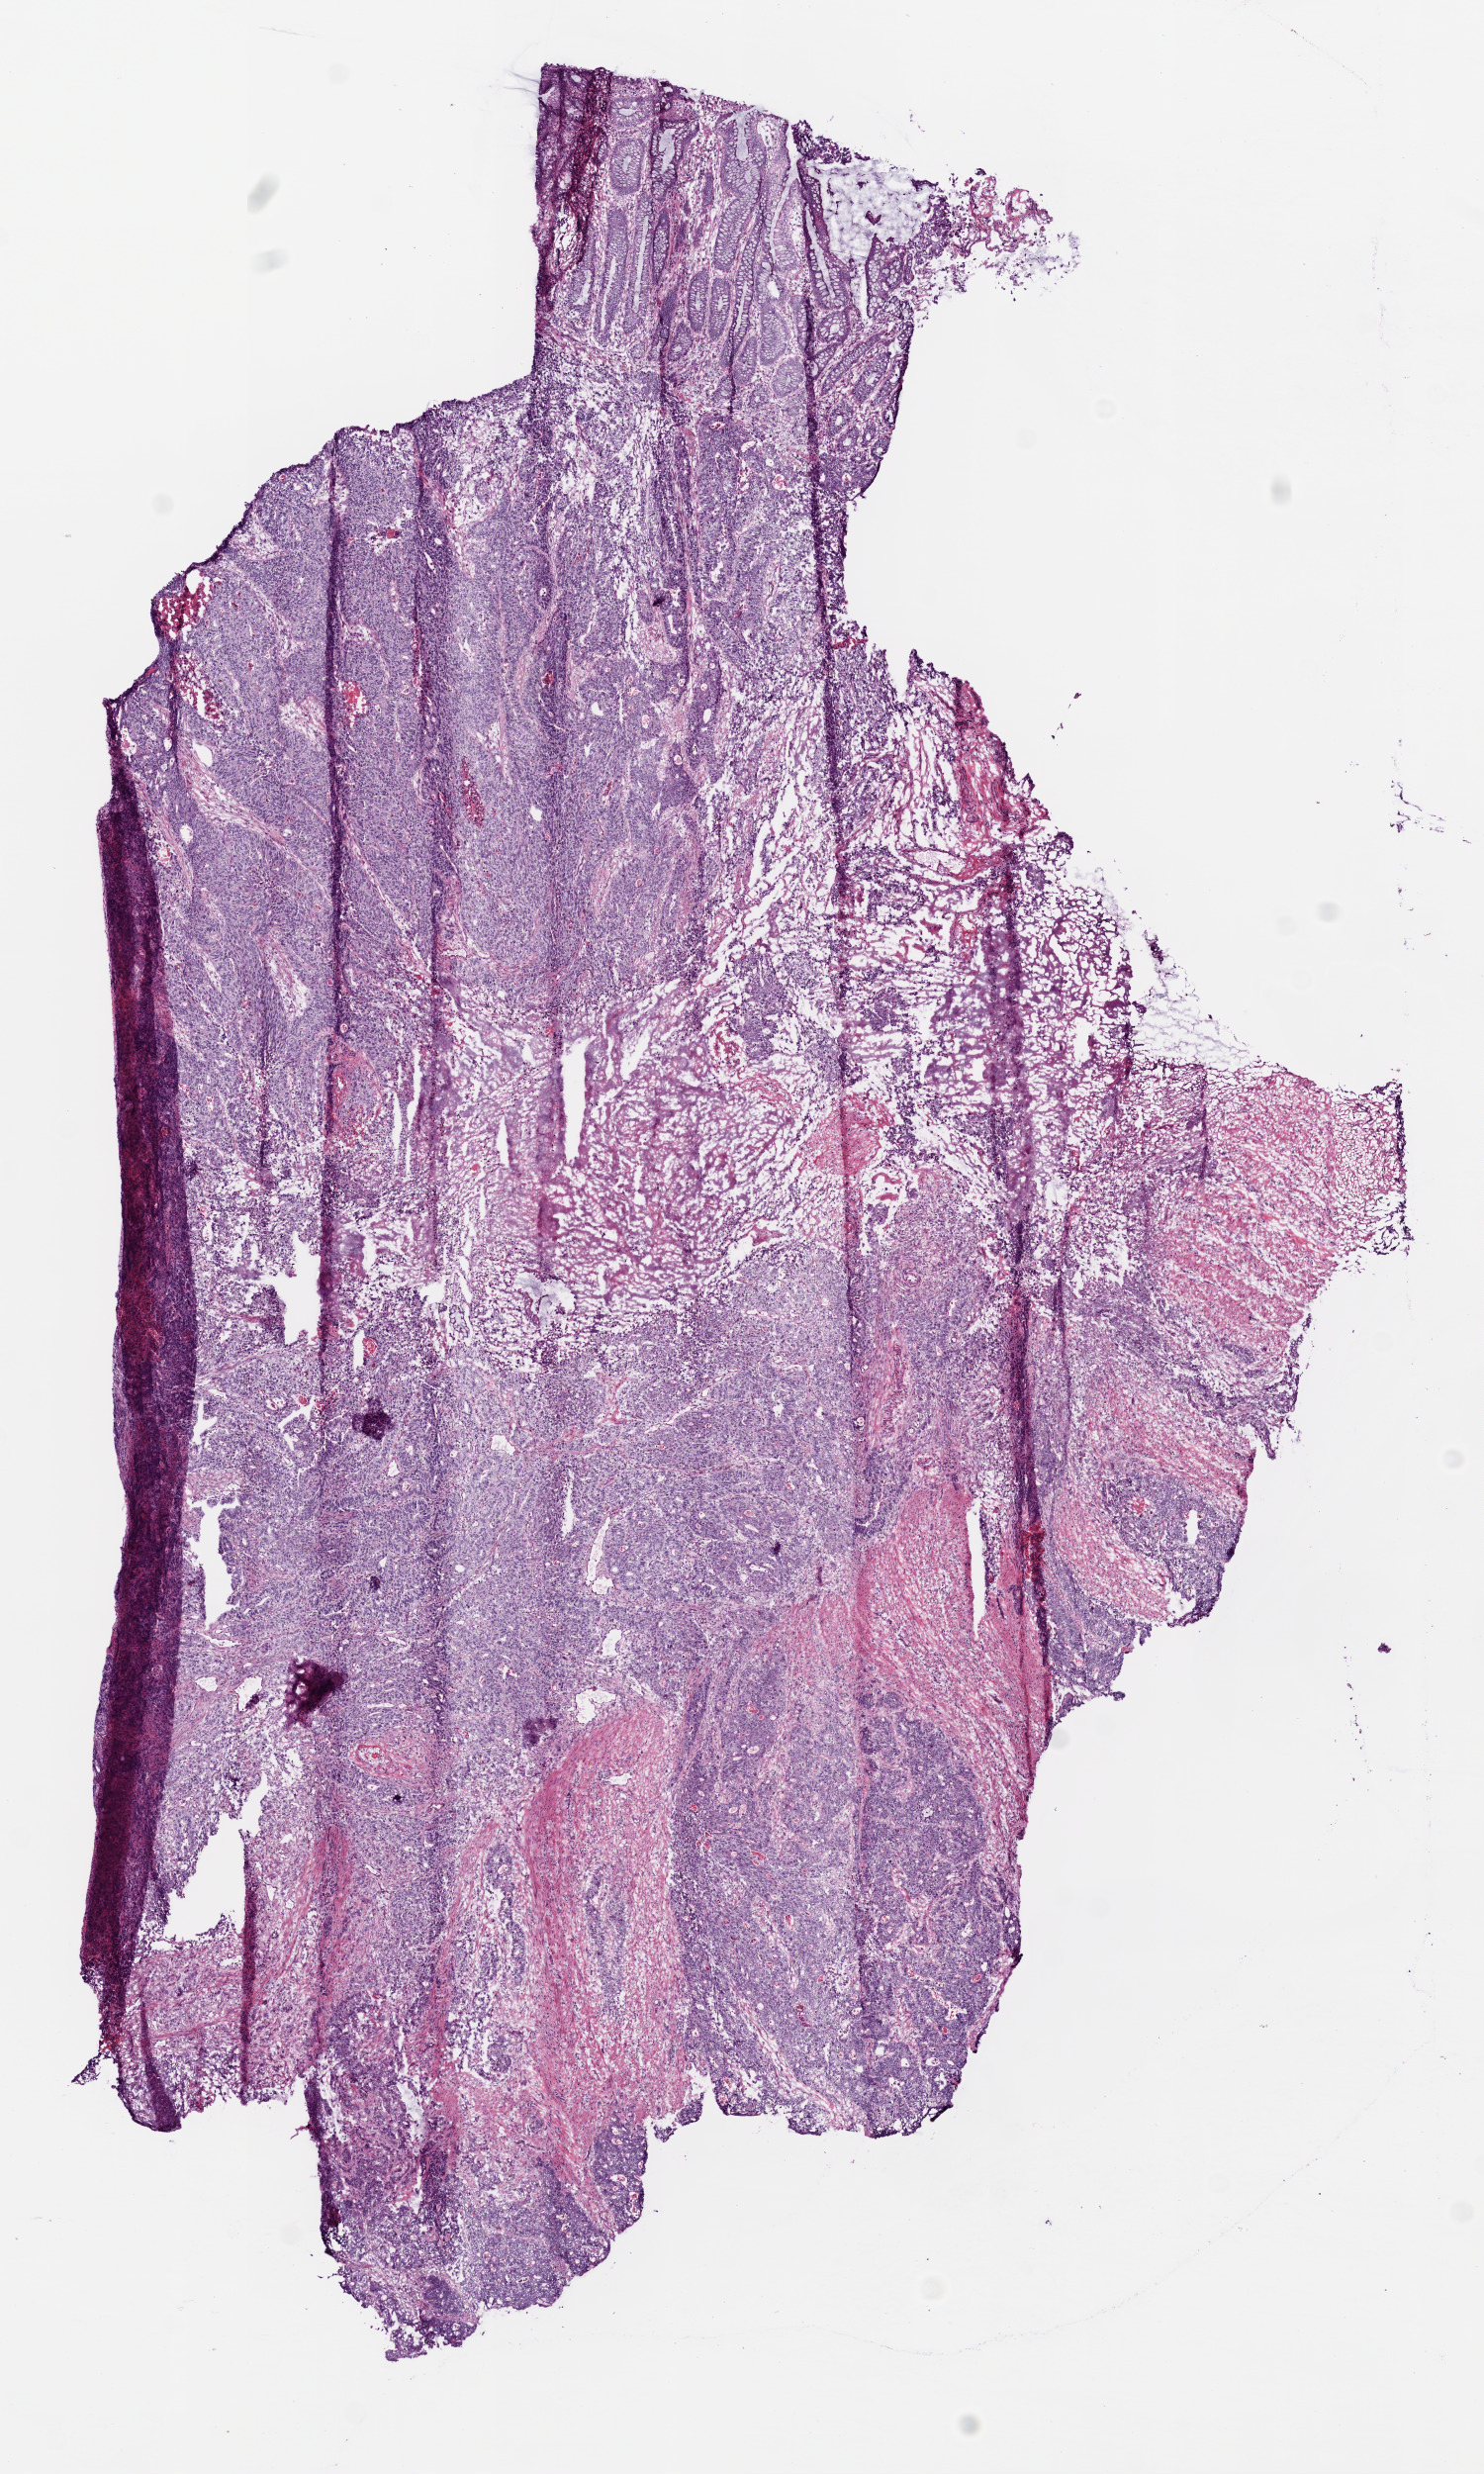
Digitized H&E-stained tissue section (whole slide) — low-resolution overview of the scanned area, about 6.0 x 10.0 mm (from a 20x scan). Frozen section from the bottom of the tissue portion. Primary tumour sample from the rectum. Female patient; age at initial diagnosis 61 years. Composition of this section per pathologist review: tumour cells 65%, tumour nuclei 75%, normal cells 10%, stromal cells 20%, necrosis 5%.
TNM: T3 N2 M0. Diagnosis: Adenocarcinoma, NOS (rectosigmoid junction). AJCC pathologic stage: IIIC (6th edition).